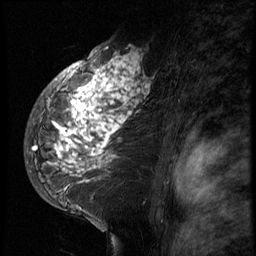
Breast MRI (dynamic contrast-enhanced), one sagittal slice. Slice 45 of 66 in the series (ordered by position). 3 images stored at this slice position (order not interpretable as contrast timing). 1.5 T. TE 4.2 ms, TR 8.9 ms. 256 × 256 image matrix, field of view 200 × 200 mm. Female patient, age 39 years. Case-level facts recorded for this patient, not image findings: setting: breast cancer imaged before/during neoadjuvant chemotherapy; receptor status: HER2-positive.
Structures marked on this image (semi-automatic segmentation, software-assisted and operator-edited):
- analysis volume of interest (the breast-tissue region the enhancement analysis was run in; not a lesion): bounding box (x1, y1, x2, y2) in pixels: (29, 44, 166, 196)
- tumour enhancement mask (voxels above the 140 % enhancement threshold inside the analysis volume of interest): (32, 47, 151, 172)